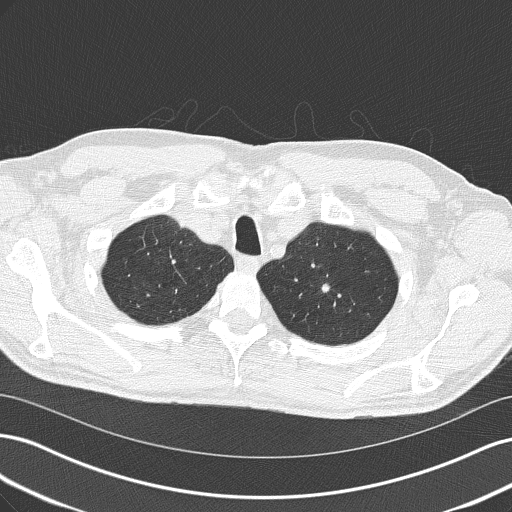
Low-dose screening chest CT, axial slice. Second screening round (one year after baseline). Lung window (W 1500 / L -600 HU). 2 mm slice thickness. Slice 36 of 185 in the series. 512 × 512 image matrix. Male, age 64 years at enrolment. Former smoker at enrolment.
- Lesion marked by an expert reader, bounding box <299,275,341,311> (left, top, right, bottom; pixels).
- The screening reader recorded 2 non-calcified nodules or masses ≥4 mm on this exam (left upper lobe, left upper lobe); which of them this box marks is not recorded.
- Official screen result: positive, no significant change: stable abnormalities potentially related to lung cancer, unchanged since the prior screening exam.
- Later outcome: lung cancer diagnosed 482 days after this screen (after the third annual screen) — adenocarcinoma, NOS, left upper lobe, poorly differentiated (G3), stage IA (AJCC 6th edition), 10 mm at pathology.